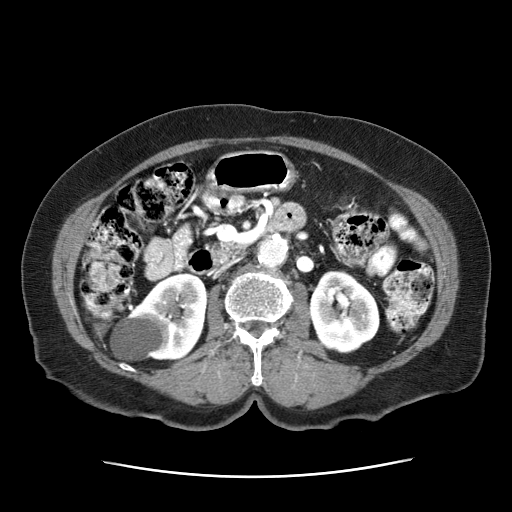
Contrast-enhanced abdominal CT (liver protocol), one axial slice. Slice 6 of 63 in the series (ordered by position). Reconstruction kernel STANDARD. 120 kVp. Intravenous contrast given. Soft-tissue window (W 400 / L 40 HU). 512 × 512 image matrix, field of view 360 × 360 mm. Patient: female, 79 years. Case-level facts recorded for this patient, not image findings: diagnosis: hepatocellular carcinoma (patient treated with transarterial chemoembolisation; whether this scan precedes or follows treatment is not stated here); TNM stage (as recorded): Stage-II.
Annotated regions visible in this slice (semi-automatically segmented with operator editing):
- abdominal aorta: bounding box (x1, y1, x2, y2) in pixels: (257, 234, 290, 267)